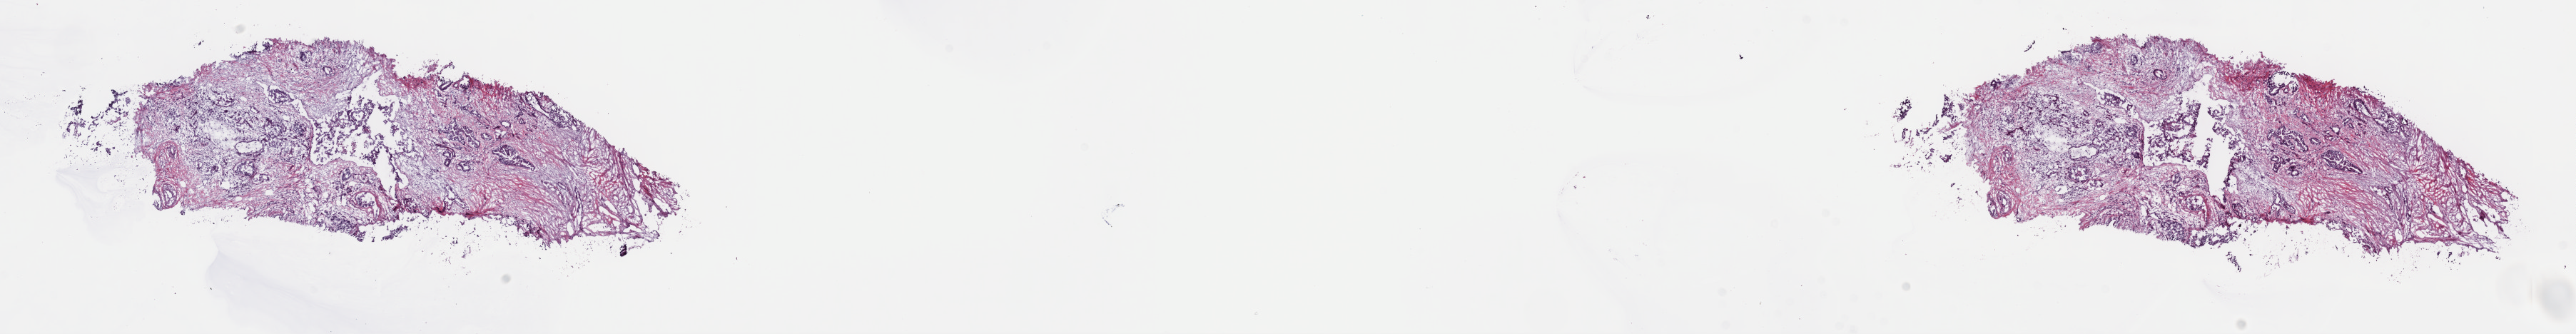
Digitized Hematoxylin and eosin (H&E) stained tissue section (whole slide), a low-resolution overview of the entire scanned area, about 29.2 x 3.8 mm. Frozen section. Primary tumour sample from the pancreas. Male patient; age at initial diagnosis 65 years.
Diagnosis: Infiltrating duct carcinoma, NOS (head of pancreas).